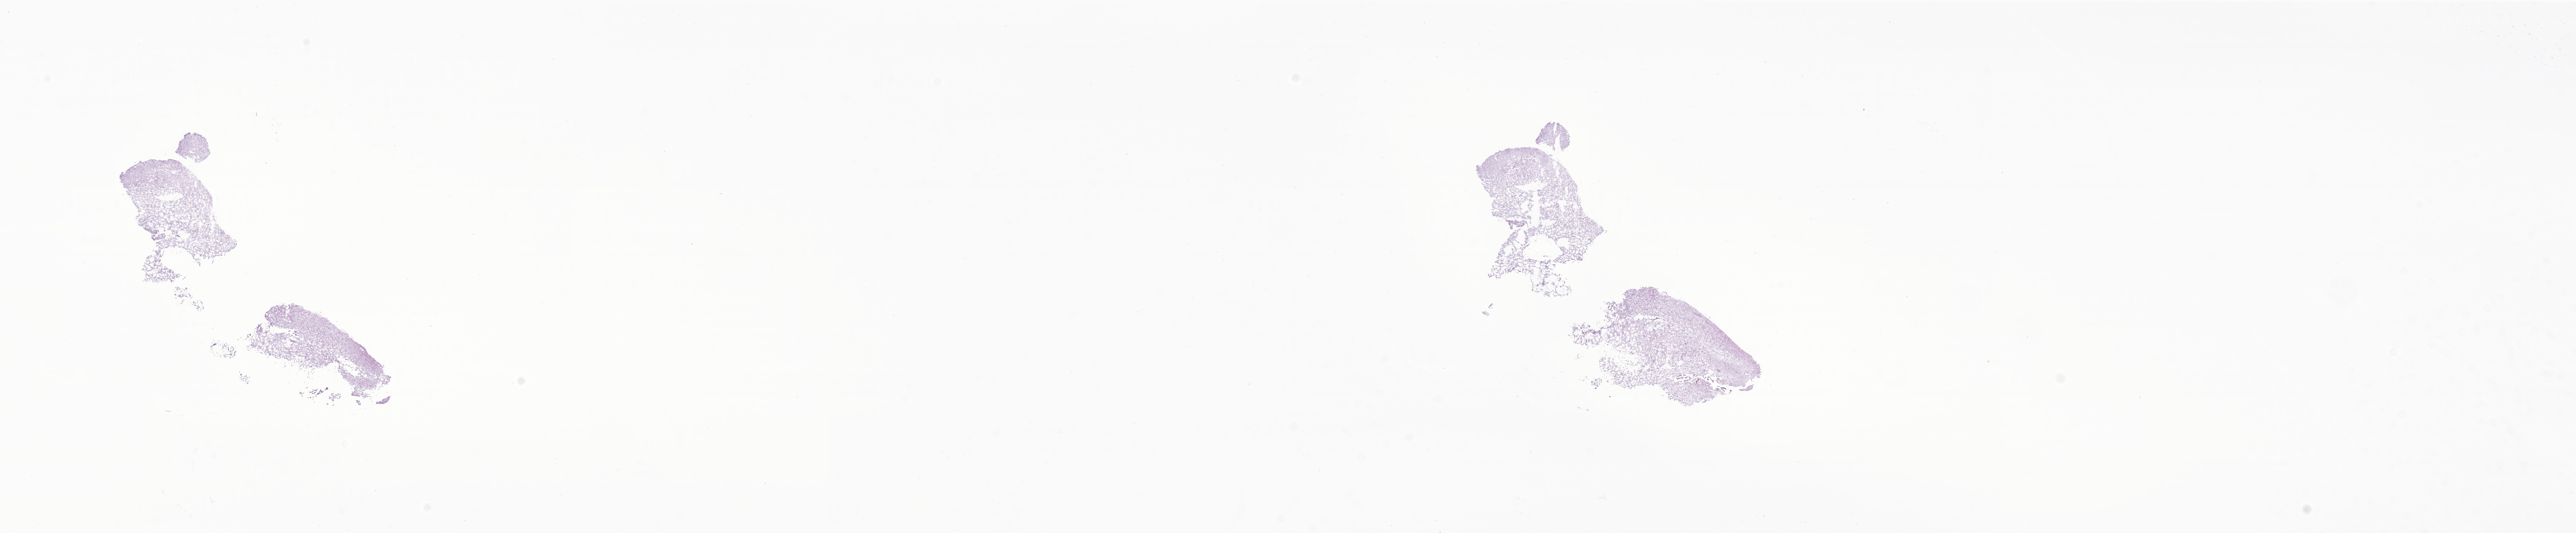
Whole-slide image, hematoxylin and eosin (H&E) stain of tumor tissue from the brain — a low-resolution overview of the entire scanned area, about 39.6 x 8.2 mm, cryosection (OCT / tissue freezing medium). Patient: male, age 65 months (5 years 5 months).
Diagnosis: Pilocytic astrocytoma.